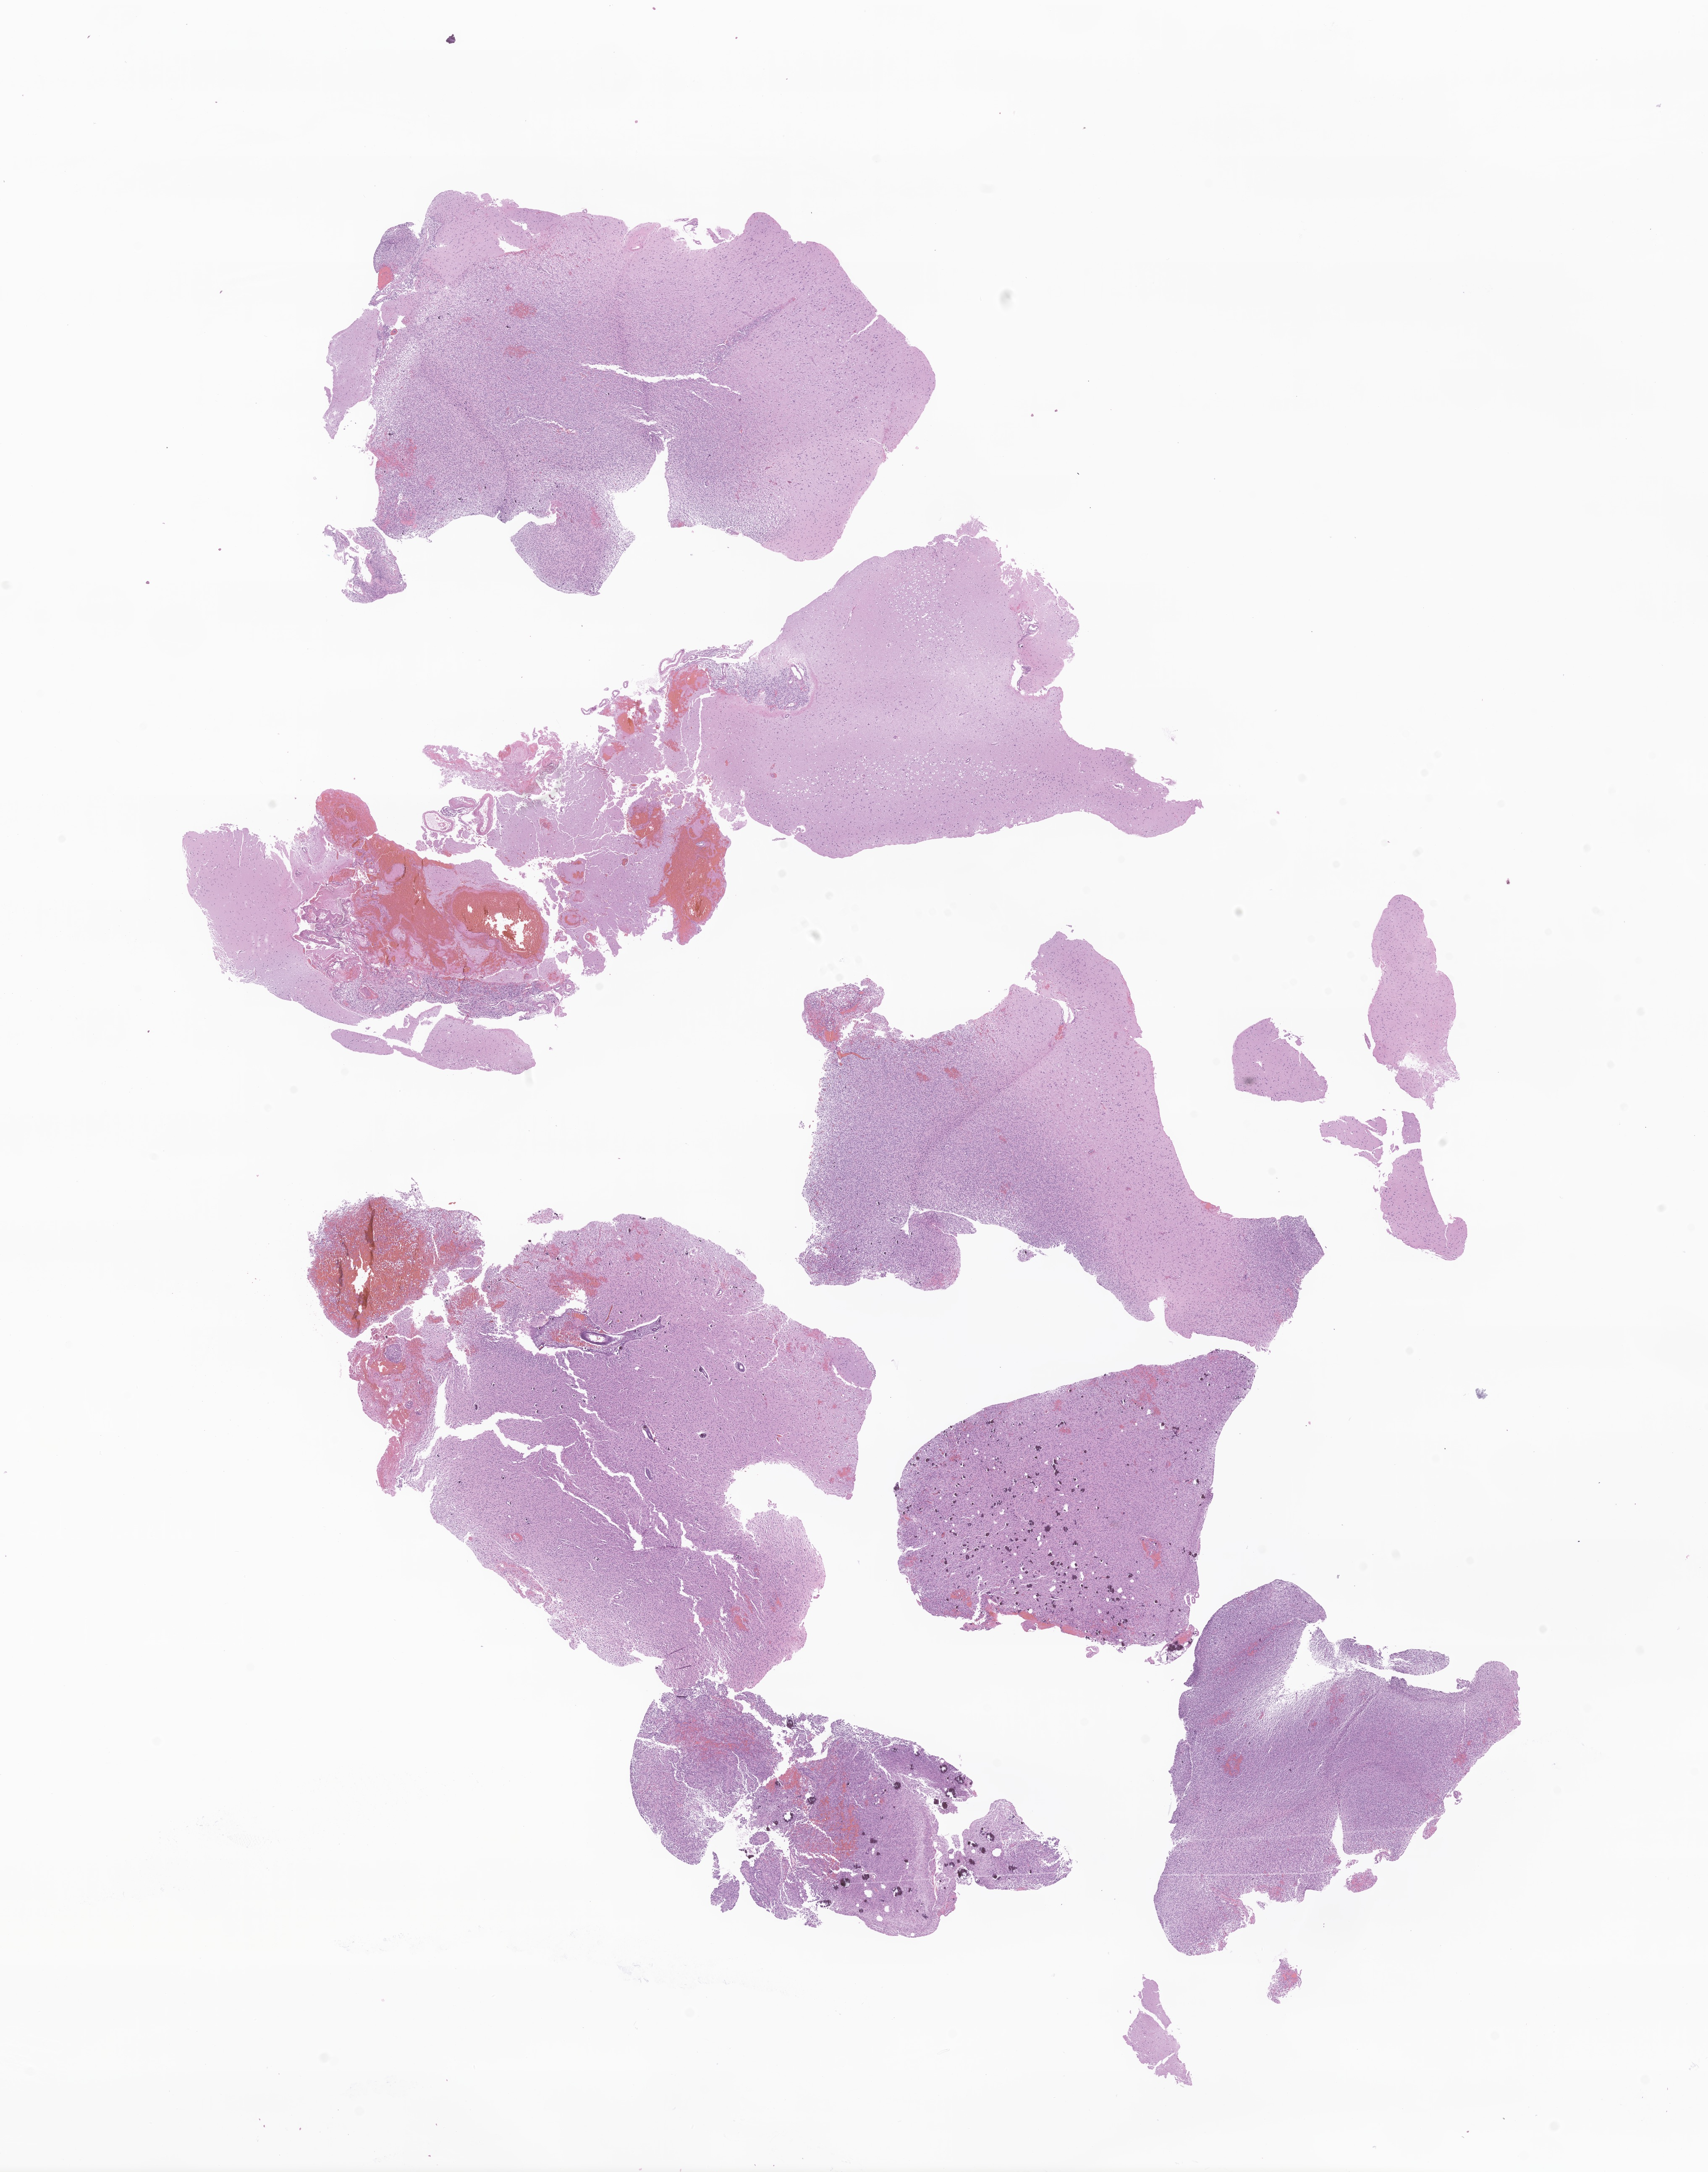
Whole-slide image, haematoxylin and eosin stain of tumor tissue from the brain, whole scanned area (about 17.1 x 21.8 mm) shown as a low-resolution overview, formalin-fixed, paraffin-embedded (FFPE) tissue. Female patient, age 46 months (3 years 10 months).
Diagnosis: Glioma, malignant.